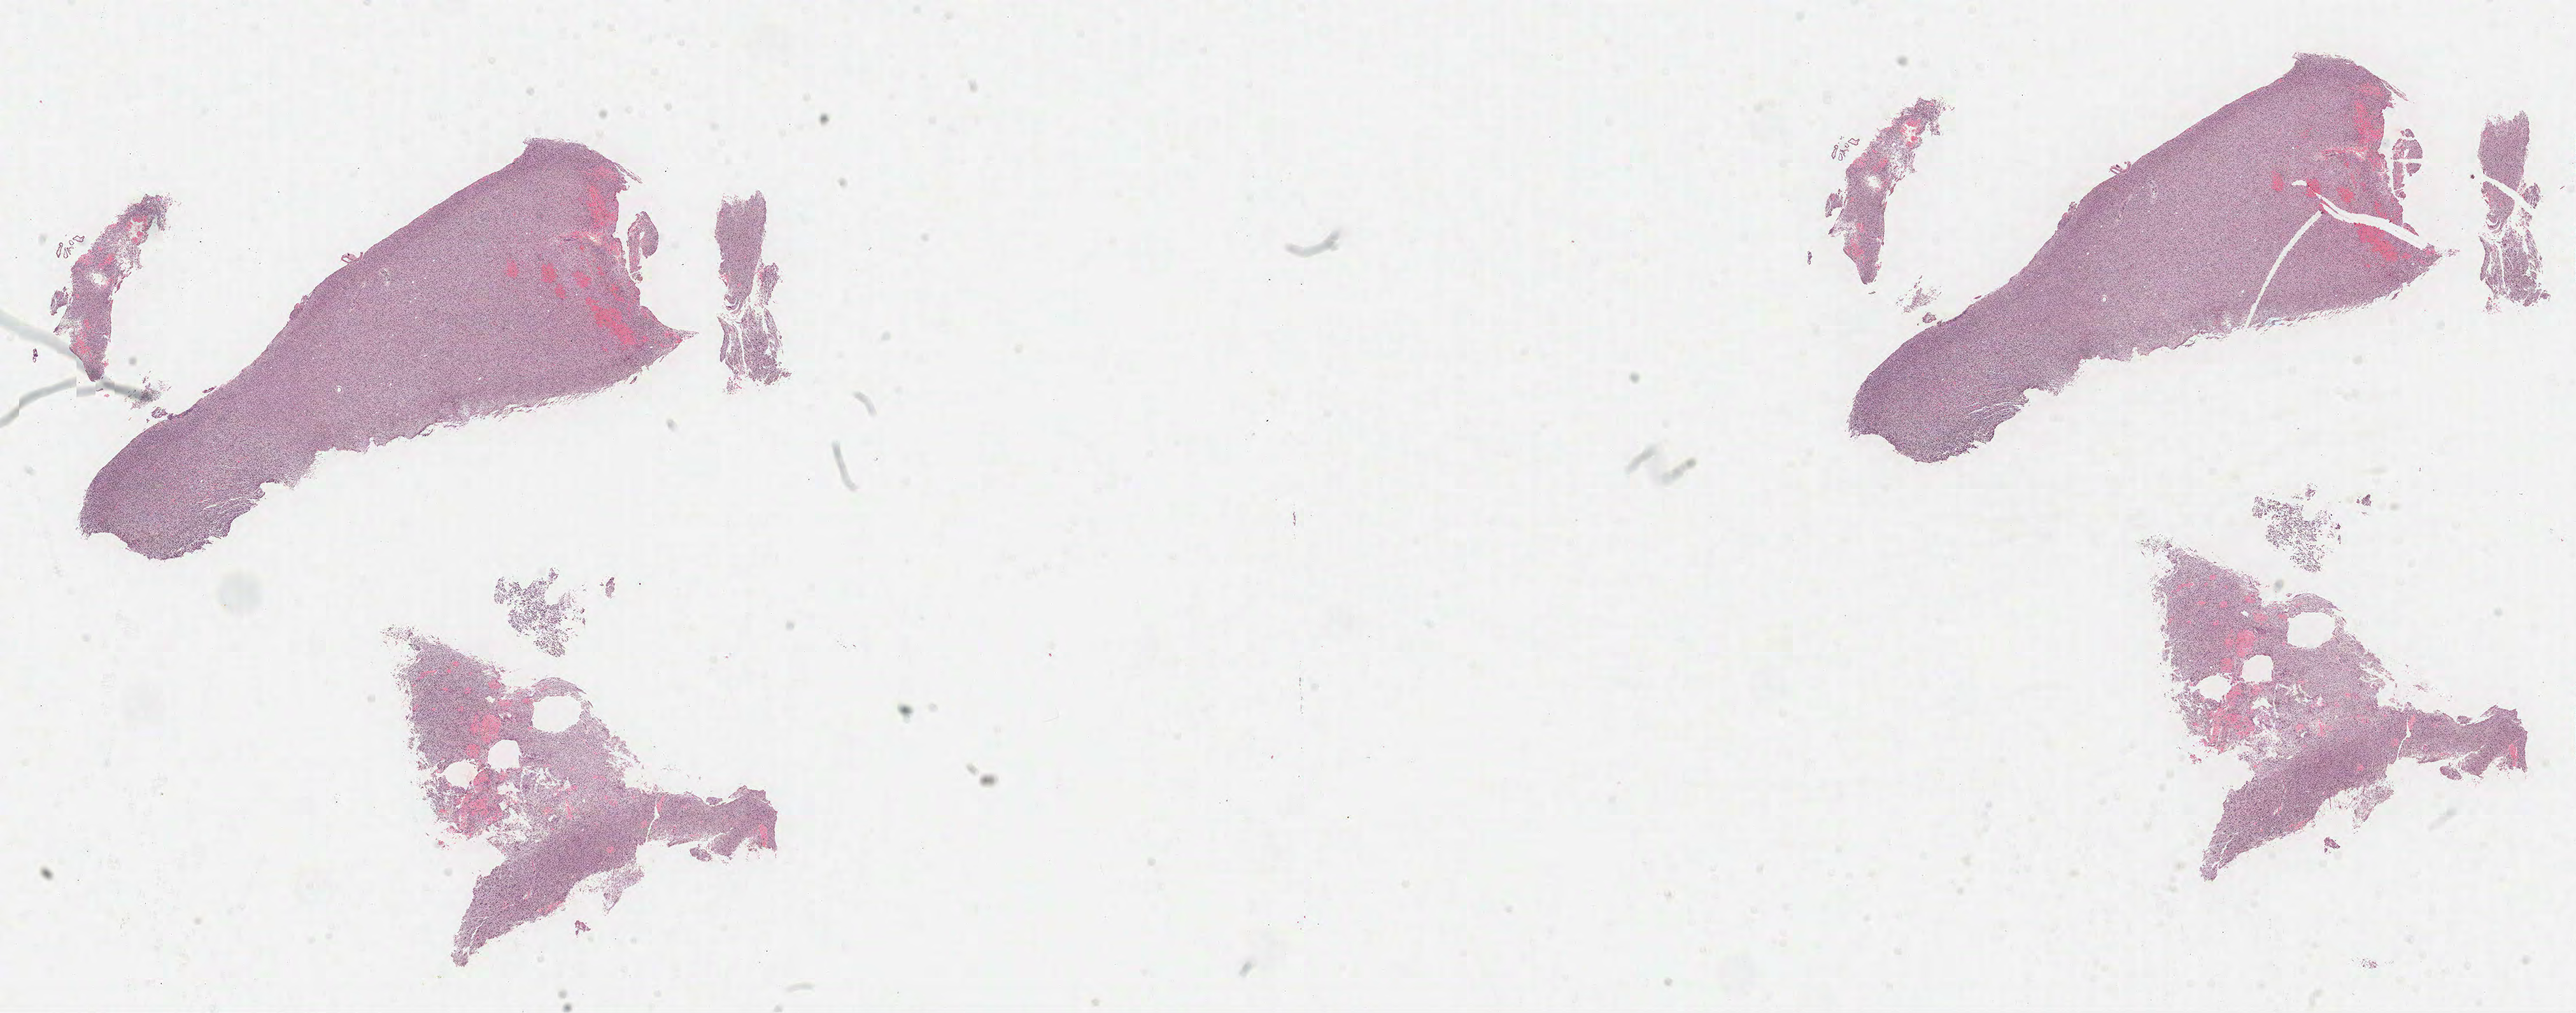
Whole-slide histology image, H&E — a low-resolution overview of the entire scanned area, about 32.6 x 12.8 mm (acquisition: 40x scan), formalin-fixed paraffin-embedded (FFPE) diagnostic section, sample: primary tumour, brain. Patient: male, age at initial diagnosis 28 years. Histologic grade: G2 (moderately differentiated).
* laterality: left
* pathologic diagnosis: Oligodendroglioma, NOS (cerebrum)